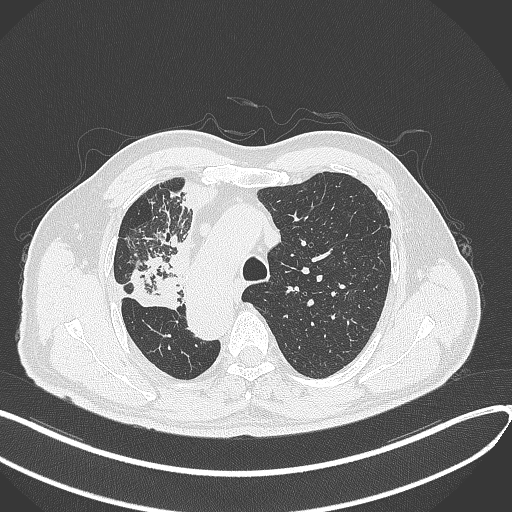
Chest CT, one axial slice. Slice 234 of 300 in the series (ordered by position). Lung window (W 1500 / L -600 HU). 1 mm slice thickness. 512 × 512 image matrix, field of view 400 × 400 mm. Male patient, age 67 years. Case-level facts recorded for this patient, not image findings: clinical TNM (as recorded): T2a N0 M0.
Annotated regions visible in this slice (rectangle marked by the reading radiologist):
- lung tumour (recorded histology: squamous cell carcinoma): bounding box (x1, y1, x2, y2) in pixels: (131, 252, 182, 312)